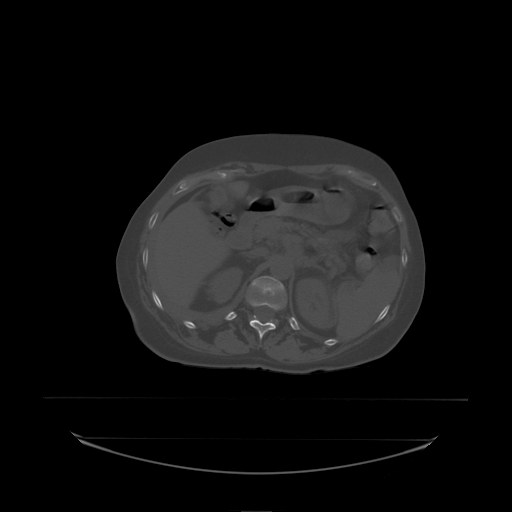
CT including the spine, one axial slice. Slice 91 of 242 in the series (ordered by position). Bone window (W 1800 / L 400 HU). 2.5 mm slice thickness. 512 × 512 image matrix, field of view 500 × 500 mm. Female patient, age 53 years. Case-level facts recorded for this patient, not image findings: primary cancer: lung.
Outlined on this slice (semi-automatic segmentation, software-assisted and operator-edited):
- L1 vertebra: box from (x=251, y=276) to (x=285, y=322) px
- T12 vertebra: (x=250, y=301)–(x=281, y=338)